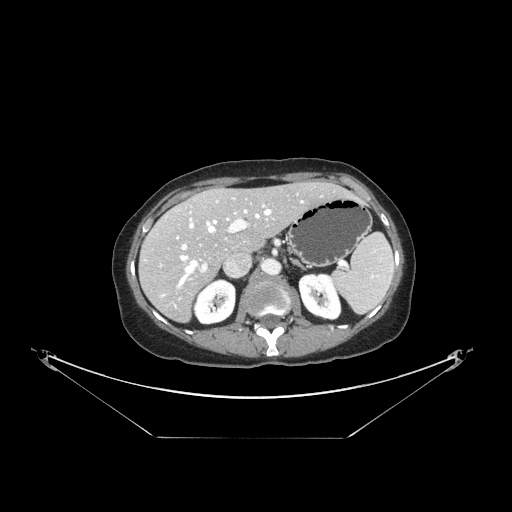
Contrast-enhanced abdominal CT, one axial slice; slice 92 of 148 in the series (ordered by position); reconstruction kernel STANDARD; intravenous contrast given; soft-tissue window (W 400 / L 40 HU); 2.5 mm slice thickness; 512 × 512 image matrix, field of view 500 × 500 mm. Female patient, age 73 years. From the clinical record (not read from this slice): diagnosis: colorectal cancer liver metastases, imaged before liver resection; multiple liver metastases: no; largest metastasis: 1 cm; chemotherapy before resection: yes.
Structures marked on this image (outlined manually by an expert reader):
- hepatic veins: bounding box (x1, y1, x2, y2) in pixels: (179, 201, 302, 287)
- liver: (140, 183, 350, 321)
- planned liver remnant (the part of the liver to remain after resection): (168, 183, 350, 254)
- portal vein (with intrahepatic branches): (176, 204, 265, 272)